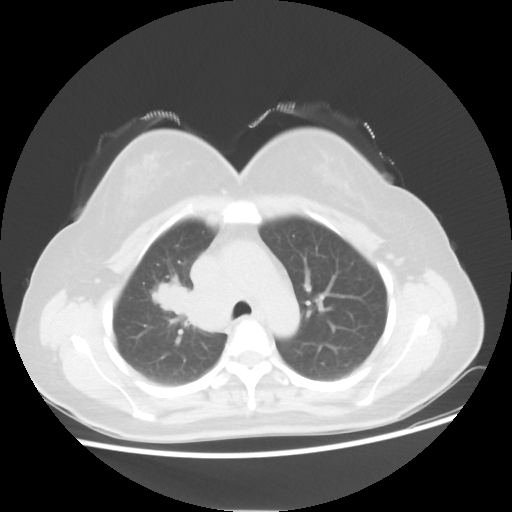
Chest CT, one axial slice; reconstruction kernel STANDARD; 100 kVp; lung window (W 1500 / L -600 HU); 5 mm slice thickness; 512 × 512 image matrix. Patient: female, 40 years. Case-level facts recorded for this patient, not image findings: clinical TNM (as recorded): T1c N3 M0.
Structures marked on this image (bounding box drawn by a radiologist):
- lung tumour (recorded histology: small cell carcinoma): bounding box (x1, y1, x2, y2) in pixels: (148, 280, 188, 321)